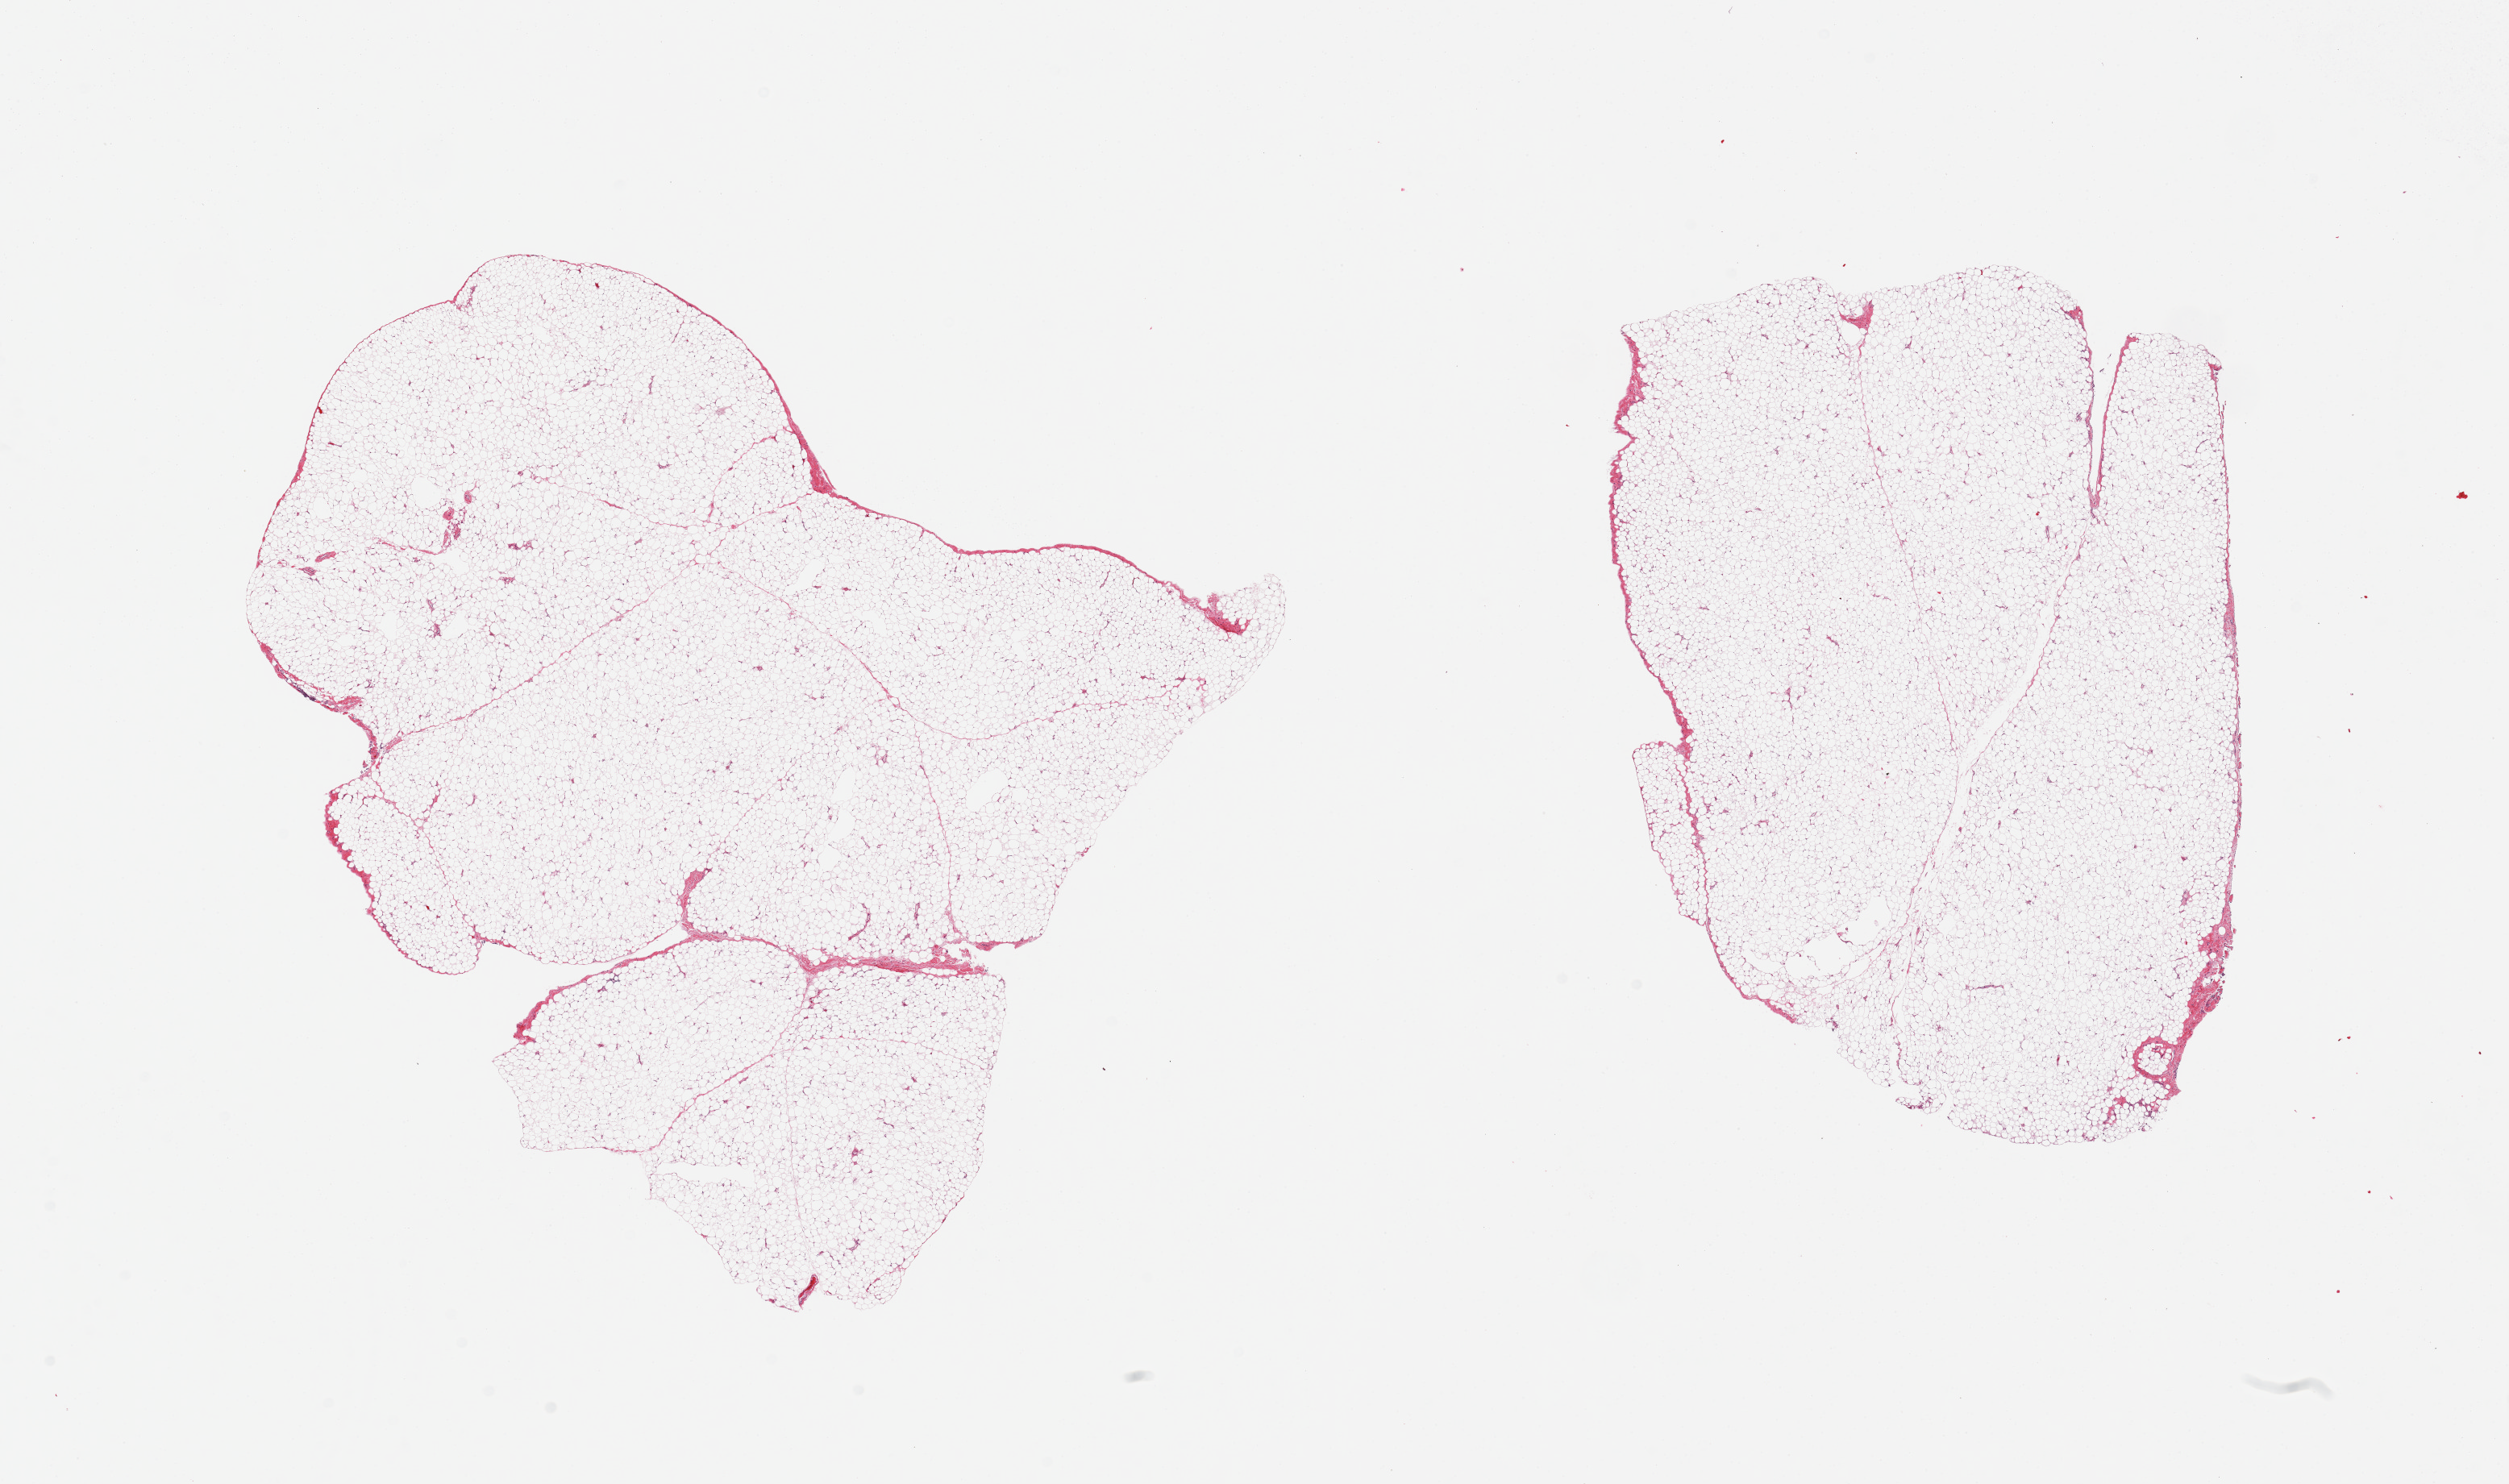
Whole-slide image, H&E stain — low-resolution overview of the scanned area, about 24.6 x 14.6 mm; PAXgene-fixed paraffin-embedded (PFPE) section; target tissue: omentum; tissue donor sample. Donor: female.
Reviewer comment on this tissue sample: 2 pieces.